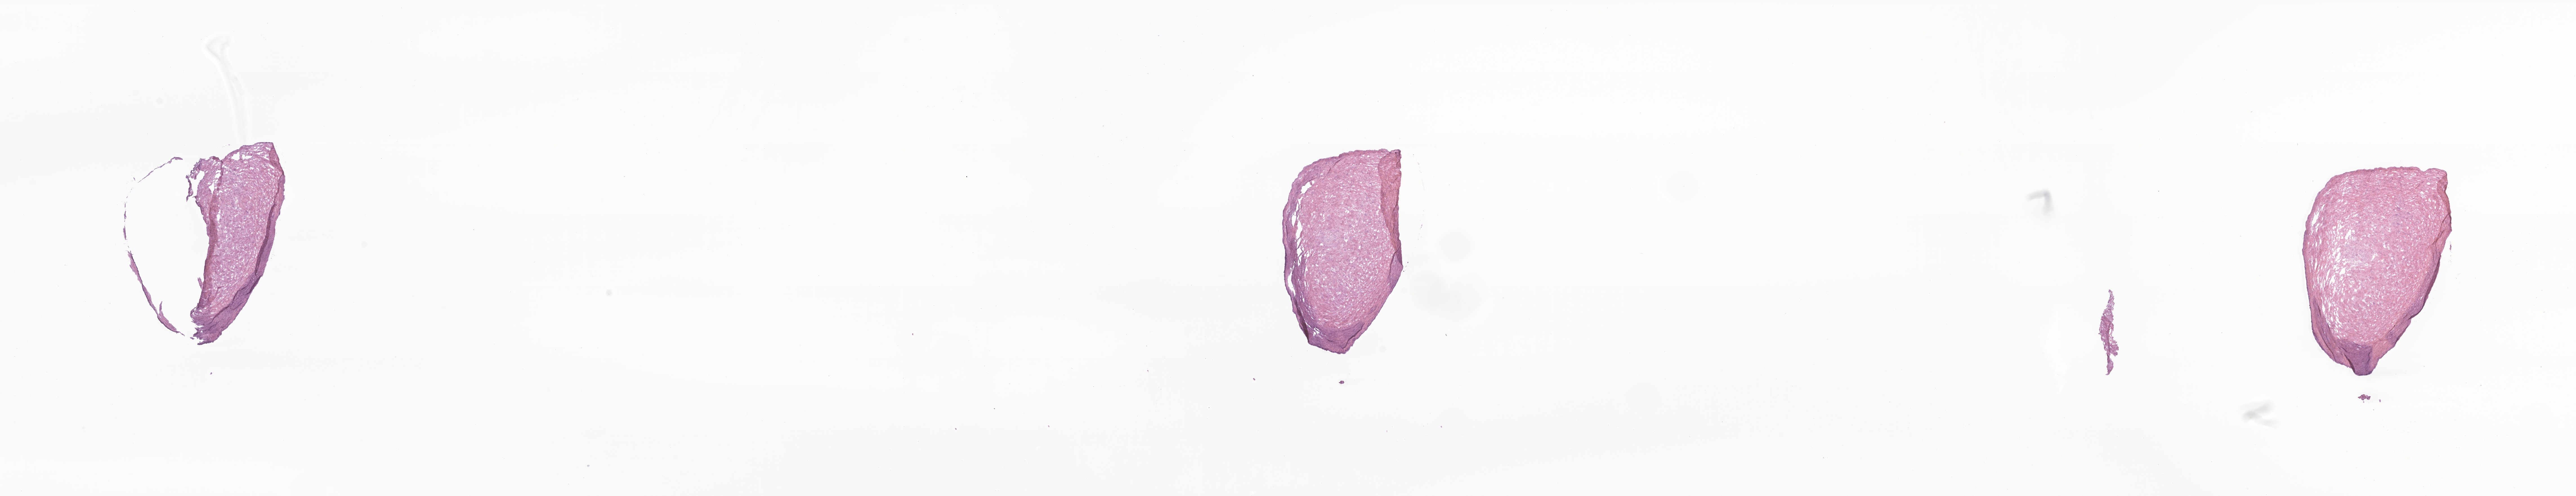
Whole-slide image, hematoxylin and eosin (H&E) stain of tumor tissue from the upper lobe of lung, low-resolution overview of the scanned area, about 38.6 x 7.4 mm, frozen section. Female patient, age 117 months (9 years 9 months).
• tissue or organ of origin (case record): upper lobe, lung
• diagnosis (ICD-O-3 morphology term): Myofibroblastic tumor, NOS